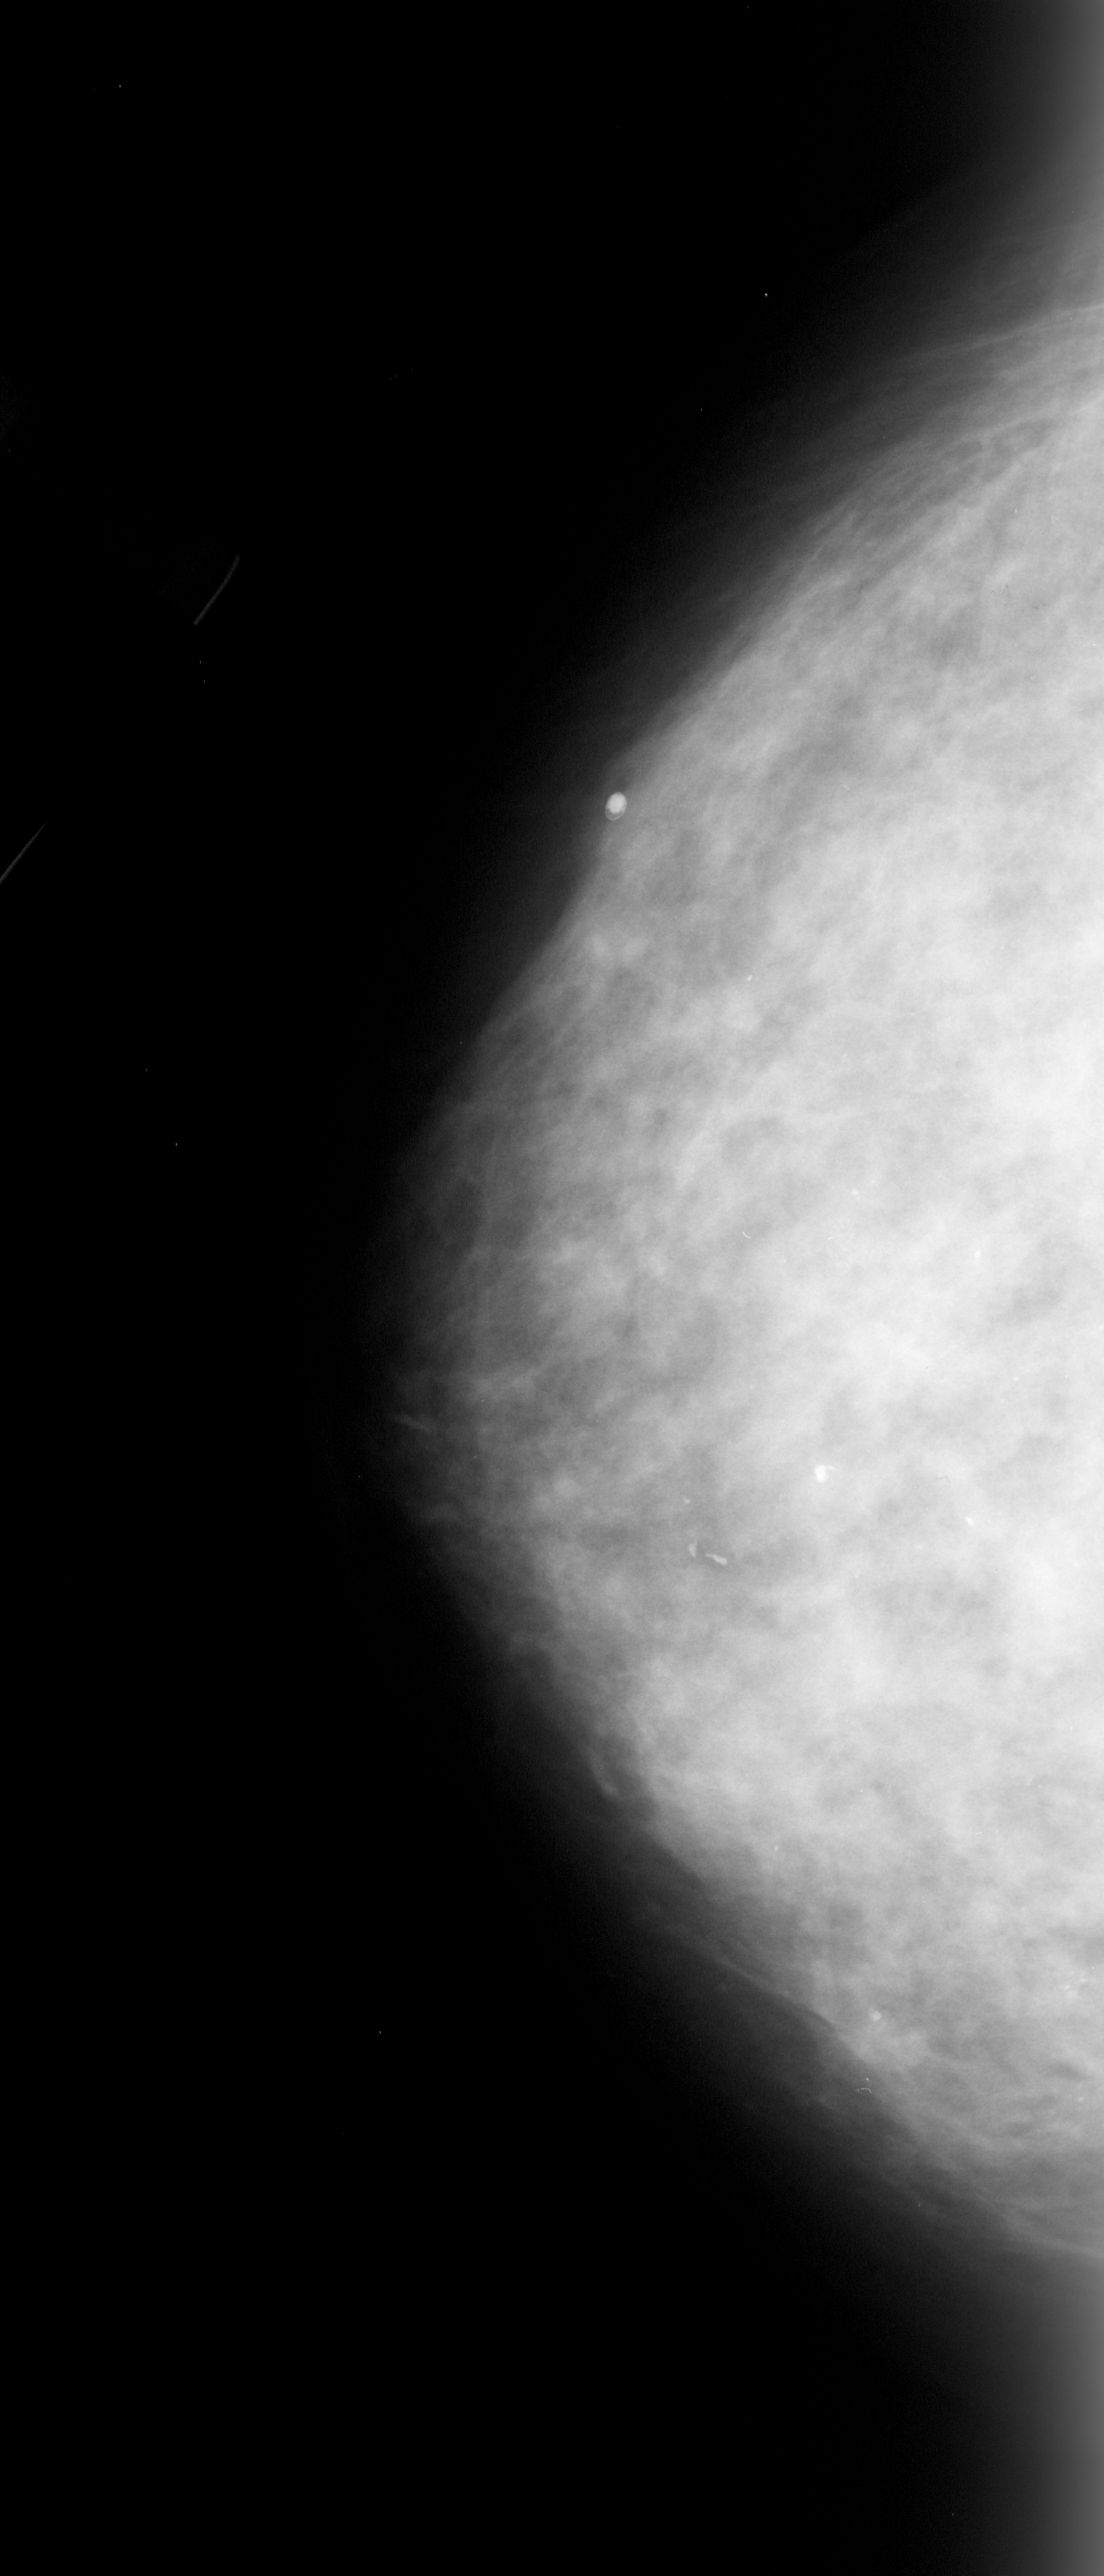
Scanned film-screen mammogram, left breast, craniocaudal (CC) view, BI-RADS breast density category 3 (scale 1–4).
- Calcifications, morphology pleomorphic, distribution segmental; BI-RADS assessment category 4; subtlety rating 3 on a 1 (subtle) to 5 (obvious) scale; pathology (as recorded): malignant.